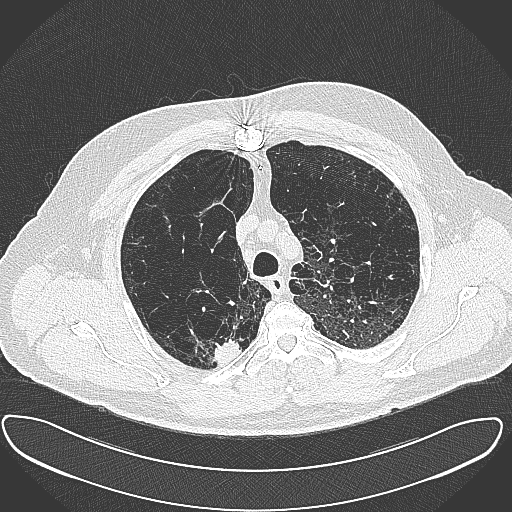
Low-dose screening chest CT, axial slice. First (baseline) screen. Lung window (W 1500 / L -600 HU). Lung (sharp) reconstruction kernel (B80f). Slice 83 of 385 in the series. Male, age 60 years at enrolment. Current smoker at enrolment.
• Lesion marked by an expert reader, box from (x=200, y=327) to (x=243, y=365) px.
• The exam's reader record, not a measurement of the box and not confirmed to be the same lesion: non-calcified nodule or mass ≥4 mm, right upper lobe, 15 × 25 mm, spiculated (stellate) margins, soft tissue attenuation.
• Official screen result: positive, change unspecified: nodule(s) >= 4 mm or enlarging nodule(s), mass(es), or other non-specific abnormalities suspicious for lung cancer.
• Lung cancer was diagnosed 32 days after this screen: carcinoma, NOS, right upper lobe, moderately differentiated (G2), stage IB (AJCC 6th edition), 35 mm at pathology.